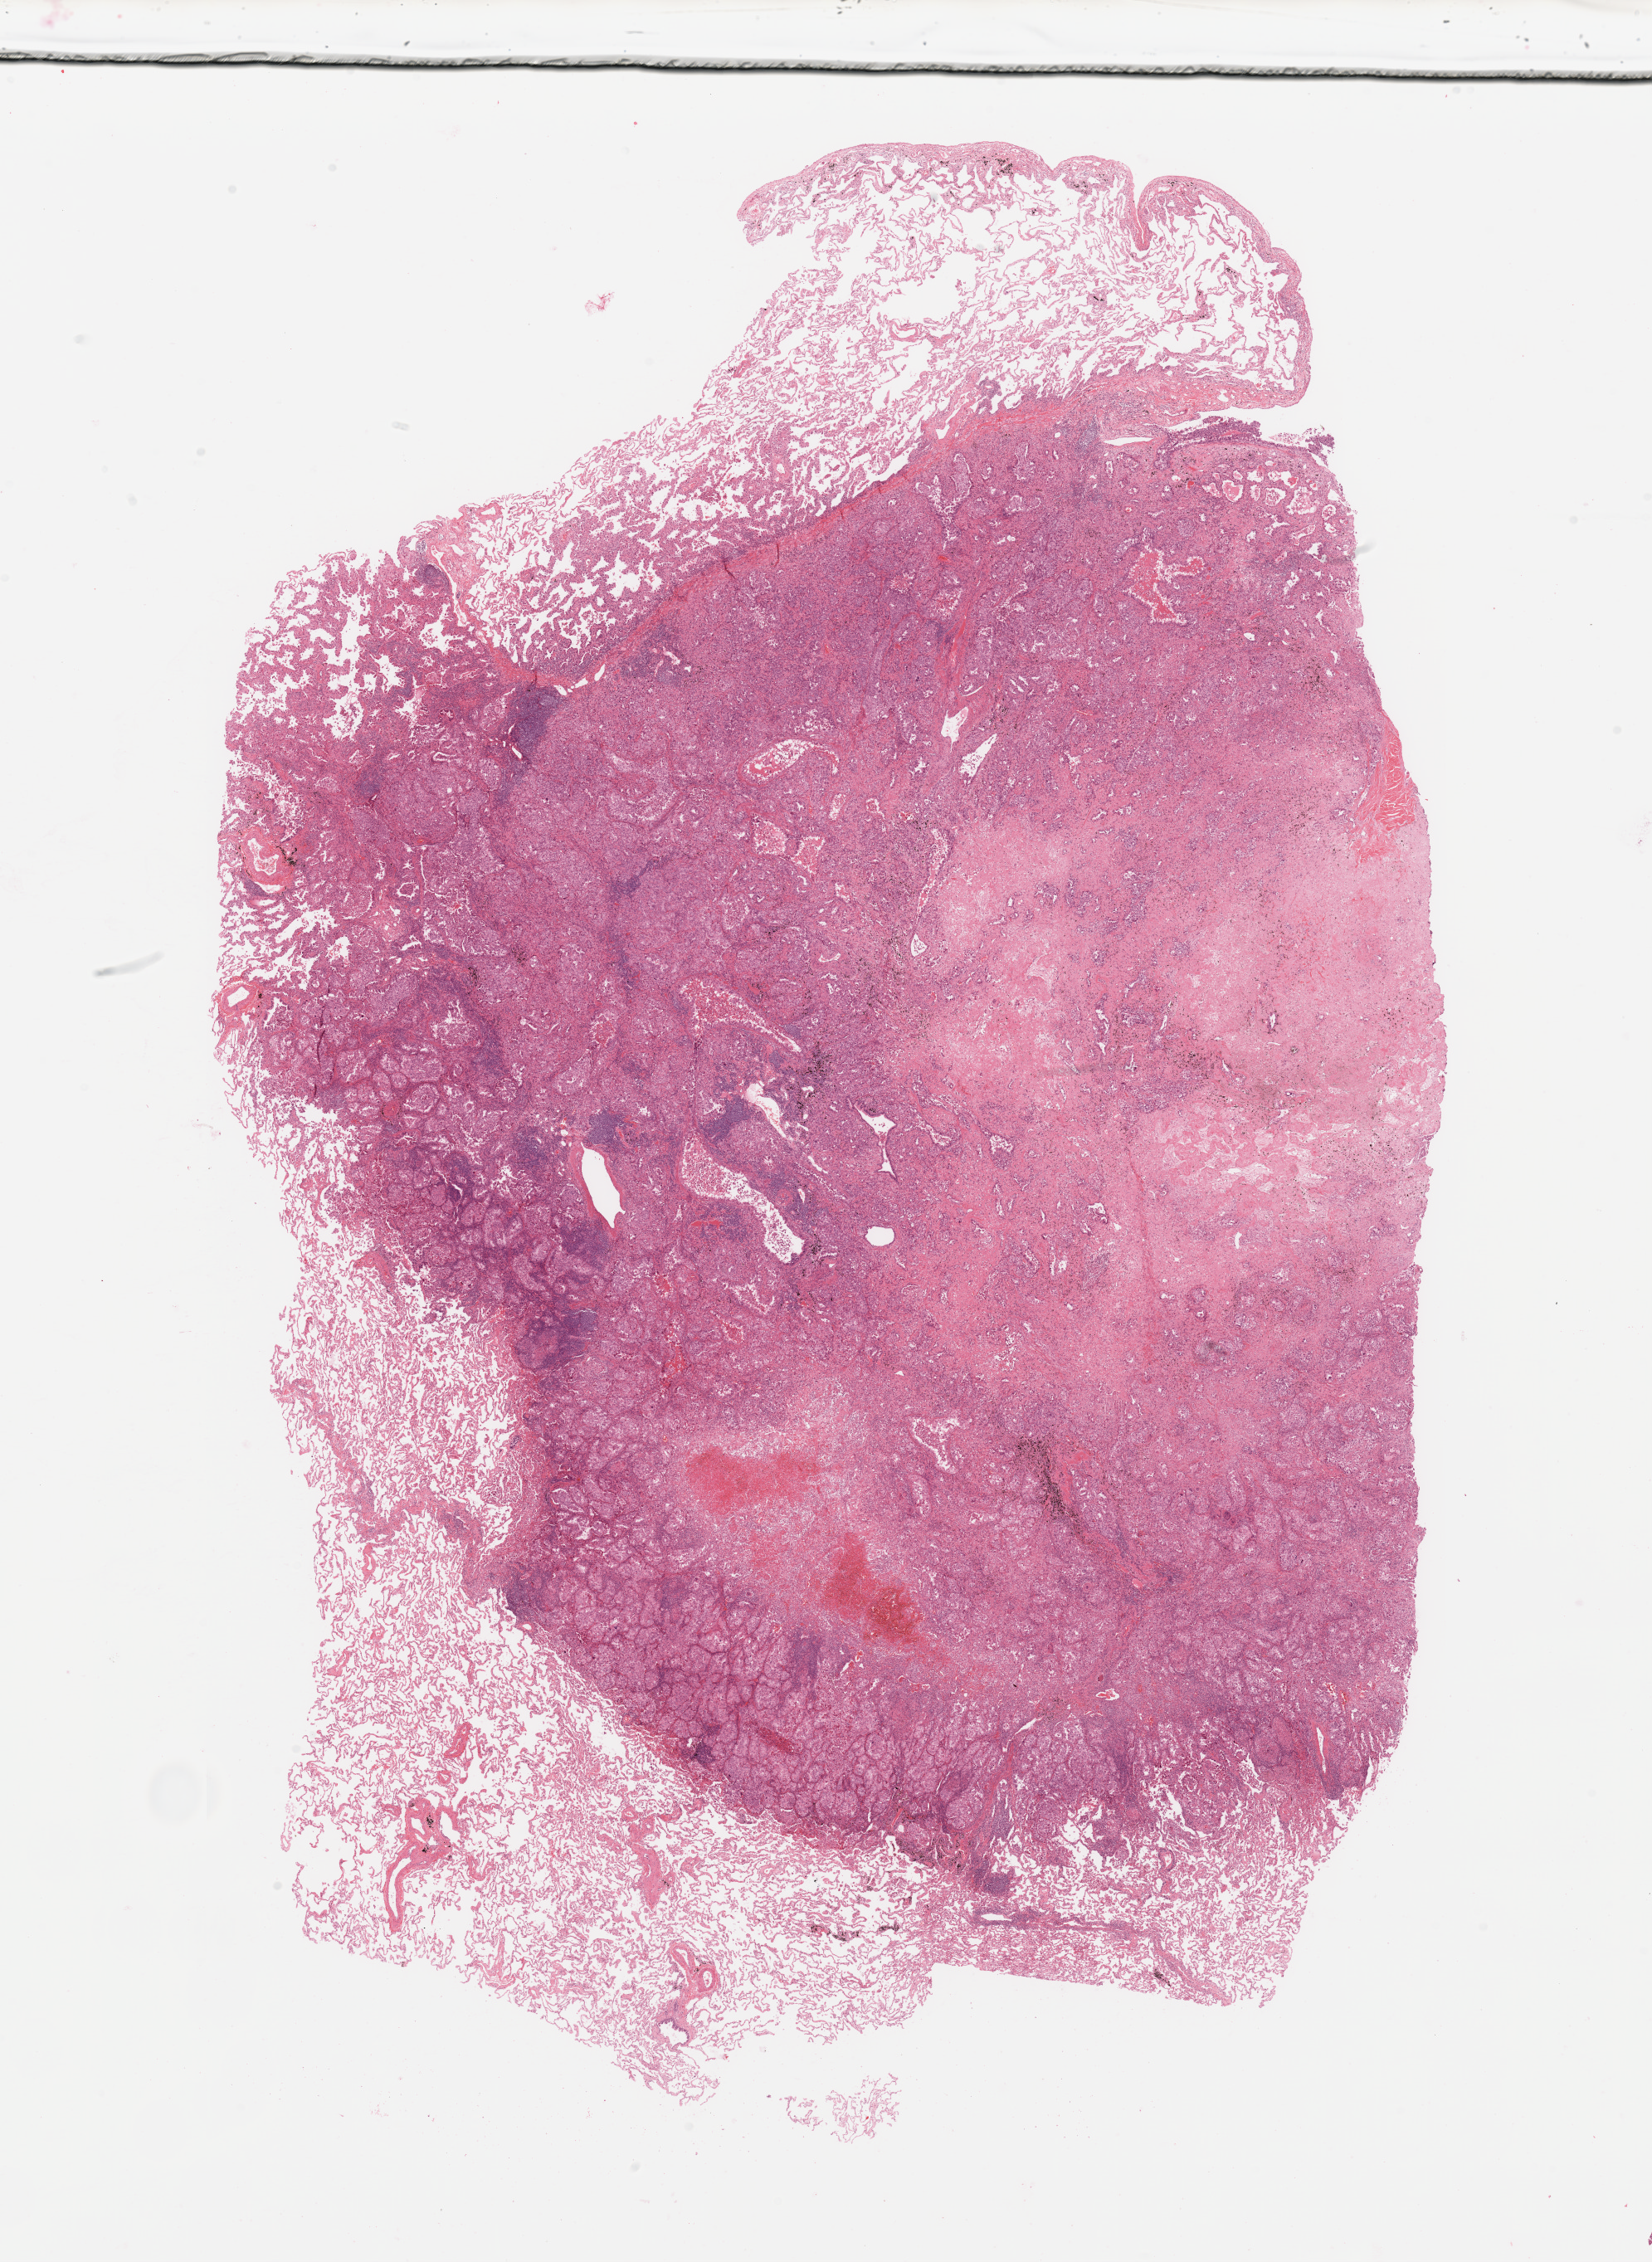
H&E whole-slide image — shown as a low-resolution overview of the whole scanned area (about 15.8 x 21.6 mm); lung, tumour tissue. Patient: female, age 62 years. Histologic grade: G3 (poorly differentiated).
Primary tumour site (as recorded): left upper lobe. AJCC pathologic stage: IB. Histologic diagnosis: Adenocarcinoma, NOS.